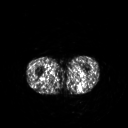
FDG PET of an extremity soft-tissue mass (from a PET/CT study), one axial slice. Position 202 of 267 along the scan axis. 3.27 mm slice thickness. 128 × 128 image matrix. Patient: male, 54 years. From the clinical record (not read from this slice): histological type: synovial sarcoma; site of the primary tumour: left poplietal fossa.
Structures marked on this image (expert contour drawn on MRI and transferred to this co-registered scan by the dataset authors):
- gross tumour volume (mass): bounding box (x1, y1, x2, y2) in pixels: (78, 82, 84, 88)